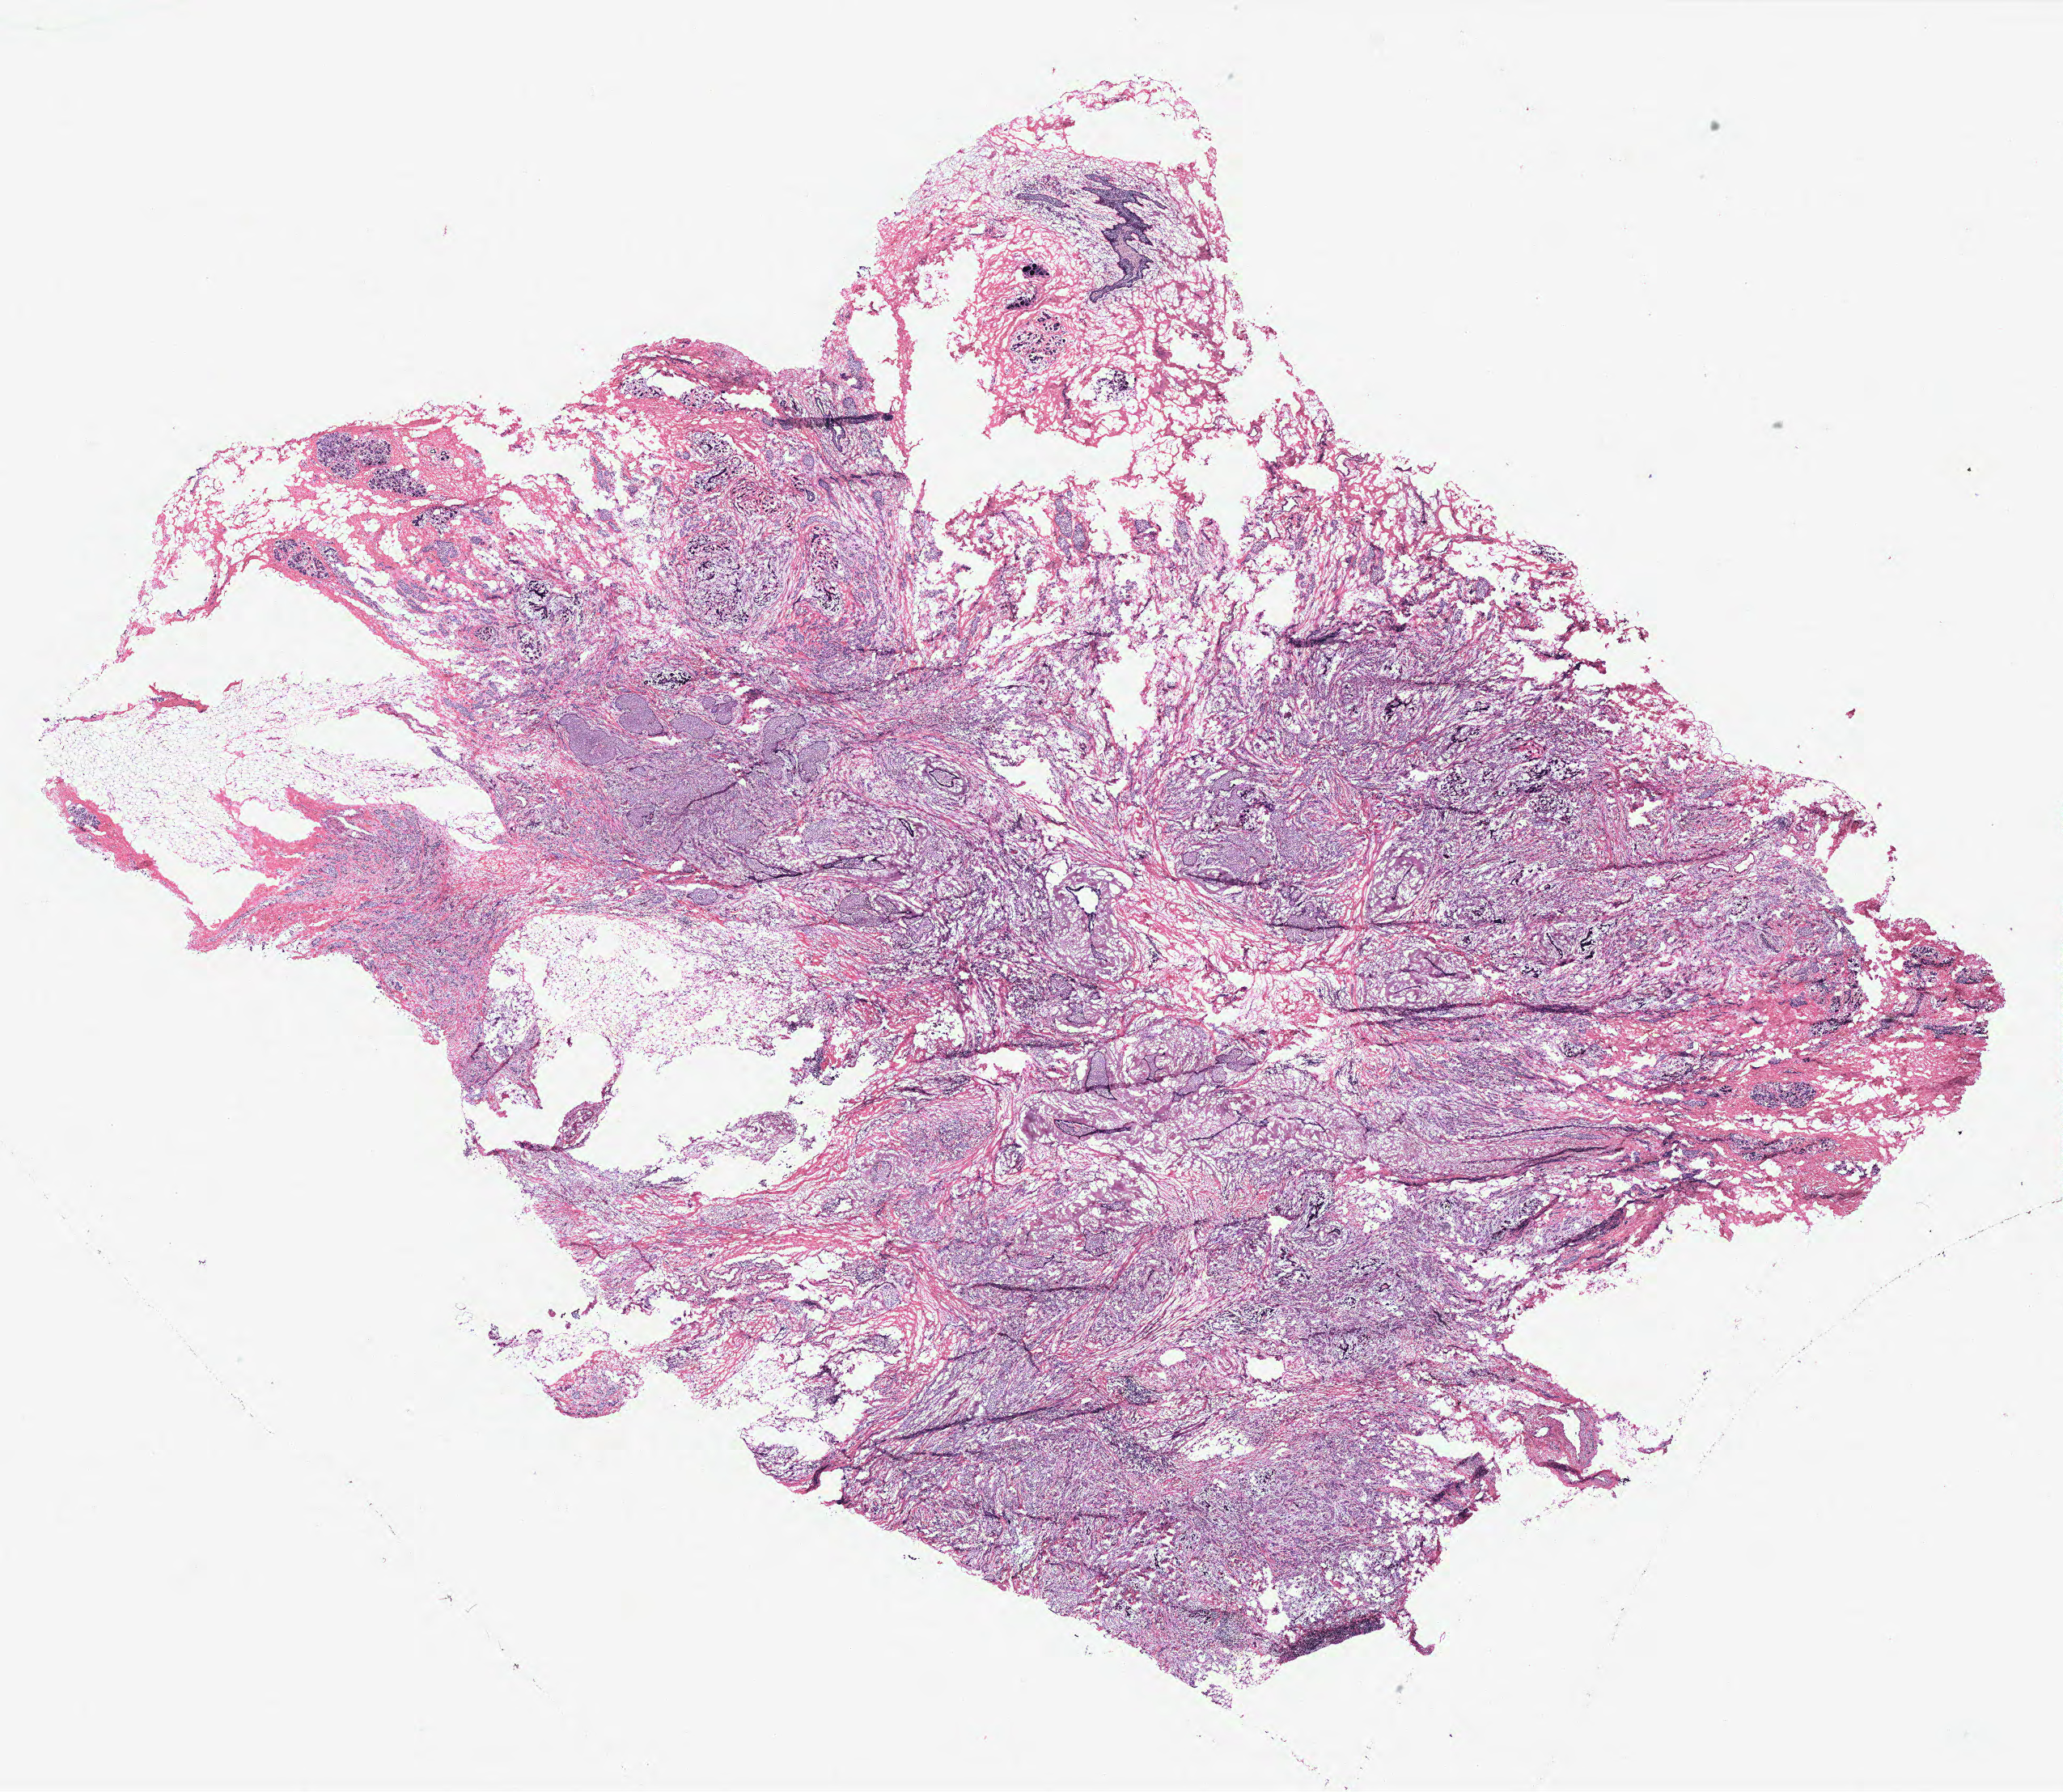
Digitized Hematoxylin and eosin (H&E) stained tissue section (whole slide) — a low-resolution overview of the entire scanned area, about 20.4 x 17.7 mm (from a 40x scan); tumour tissue sample, breast. Patient: female, age 49 years.
- AJCC pathologic stage: IIA
- diagnosis: Infiltrating lobular carcinoma, NOS